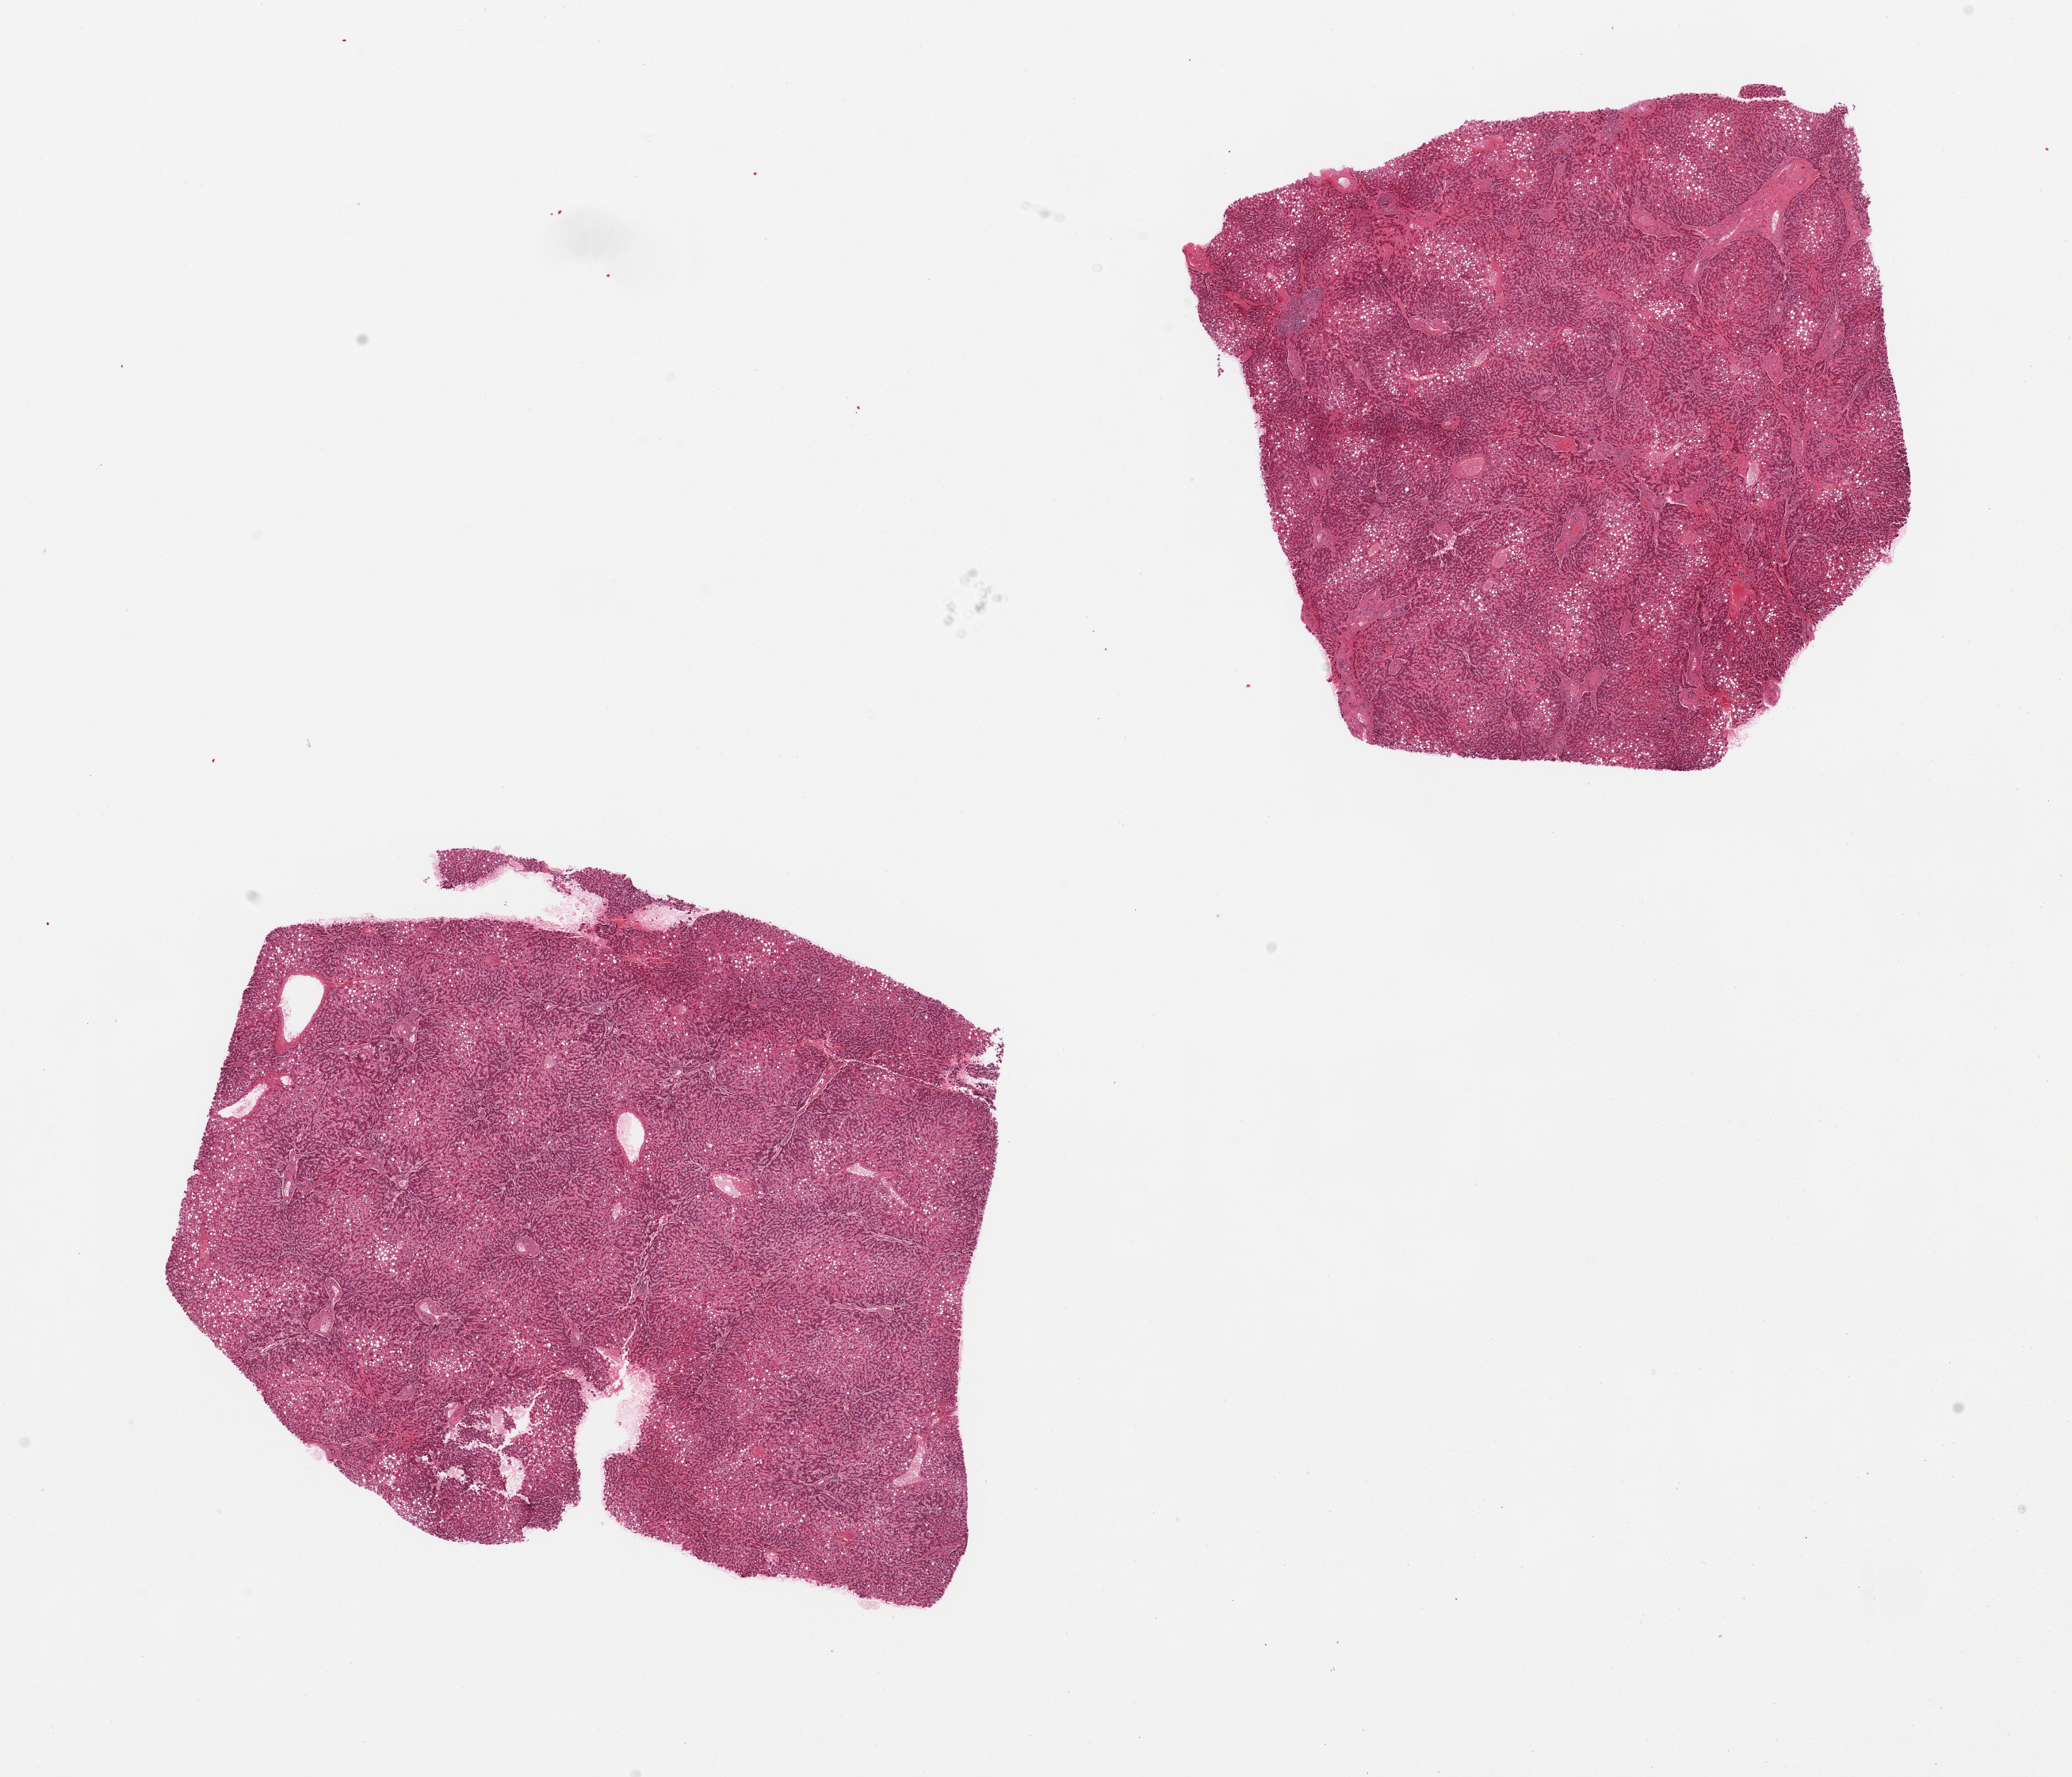
Digitized haematoxylin and eosin-stained section, shown as a low-resolution overview of the whole scanned area (about 20.7 x 17.7 mm, acquisition: 20x scan); PAXgene-fixed paraffin-embedded (PFPE) section; target tissue: liver; donor tissue sample. Female donor.
Reviewer comment on this tissue sample: 2 pieces, moderate congestions; micro and macrovesicular steatosis in ~70% of parenchyma.